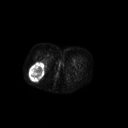
FDG PET of an extremity soft-tissue mass (from a PET/CT study), one axial slice; slice 45 of 267 in the series (ordered by position); 128 × 128 image matrix, field of view 700 × 700 mm. Patient: female, 70 years. From the clinical record (not read from this slice): histological type: synovial sarcoma; grade: intermediate; site of the primary tumour: right buttock.
Structures marked on this image (expert contour drawn on MRI and transferred to this co-registered scan by the dataset authors):
- gross tumour volume including surrounding oedema: box from (x=29, y=62) to (x=45, y=81) px
- gross tumour volume (mass): (x=29, y=62)–(x=45, y=81)